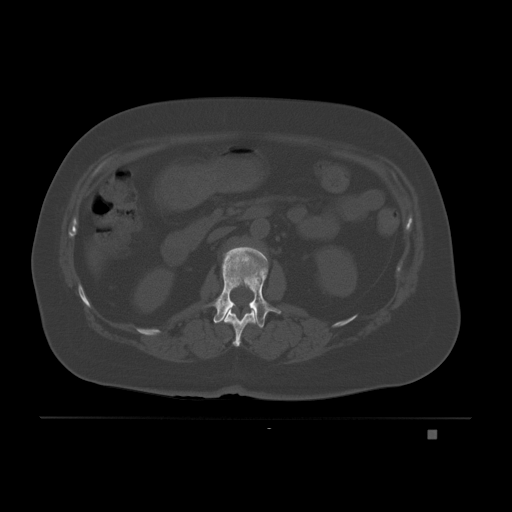
CT including the spine, one axial slice; position 72 of 221 along the scan axis; bone window (W 1800 / L 400 HU); 512 × 512 image matrix, field of view 474 × 474 mm. Female patient, age 63 years. Case-level facts recorded for this patient, not image findings: primary cancer: breast.
Structures marked on this image (semi-automatic segmentation, software-assisted and operator-edited):
- L1 vertebra: bounding box <202,246,281,328> (left, top, right, bottom; pixels)
- T12 vertebra: <224,310,256,347>